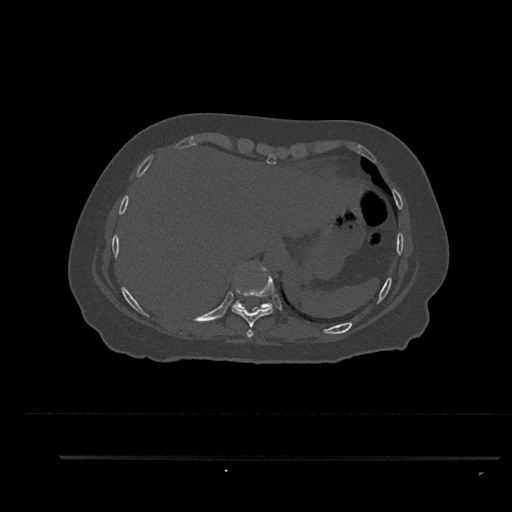
CT including the spine, one axial slice. Position 400 of 797 along the scan axis. 120 kVp. Bone window (W 1800 / L 400 HU). 512 × 512 image matrix, field of view 408 × 408 mm. Female patient, age 44 years. Case-level facts recorded for this patient, not image findings: primary cancer: renal; vertebrae with lytic lesions (as recorded): L1.
Structures marked on this image (semi-automatically segmented with operator editing):
- T10 vertebra: bounding box [x1, y1, x2, y2] px = [233, 300, 273, 310]
- T8 vertebra: [246, 329, 254, 338]
- T9 vertebra: [232, 264, 274, 328]